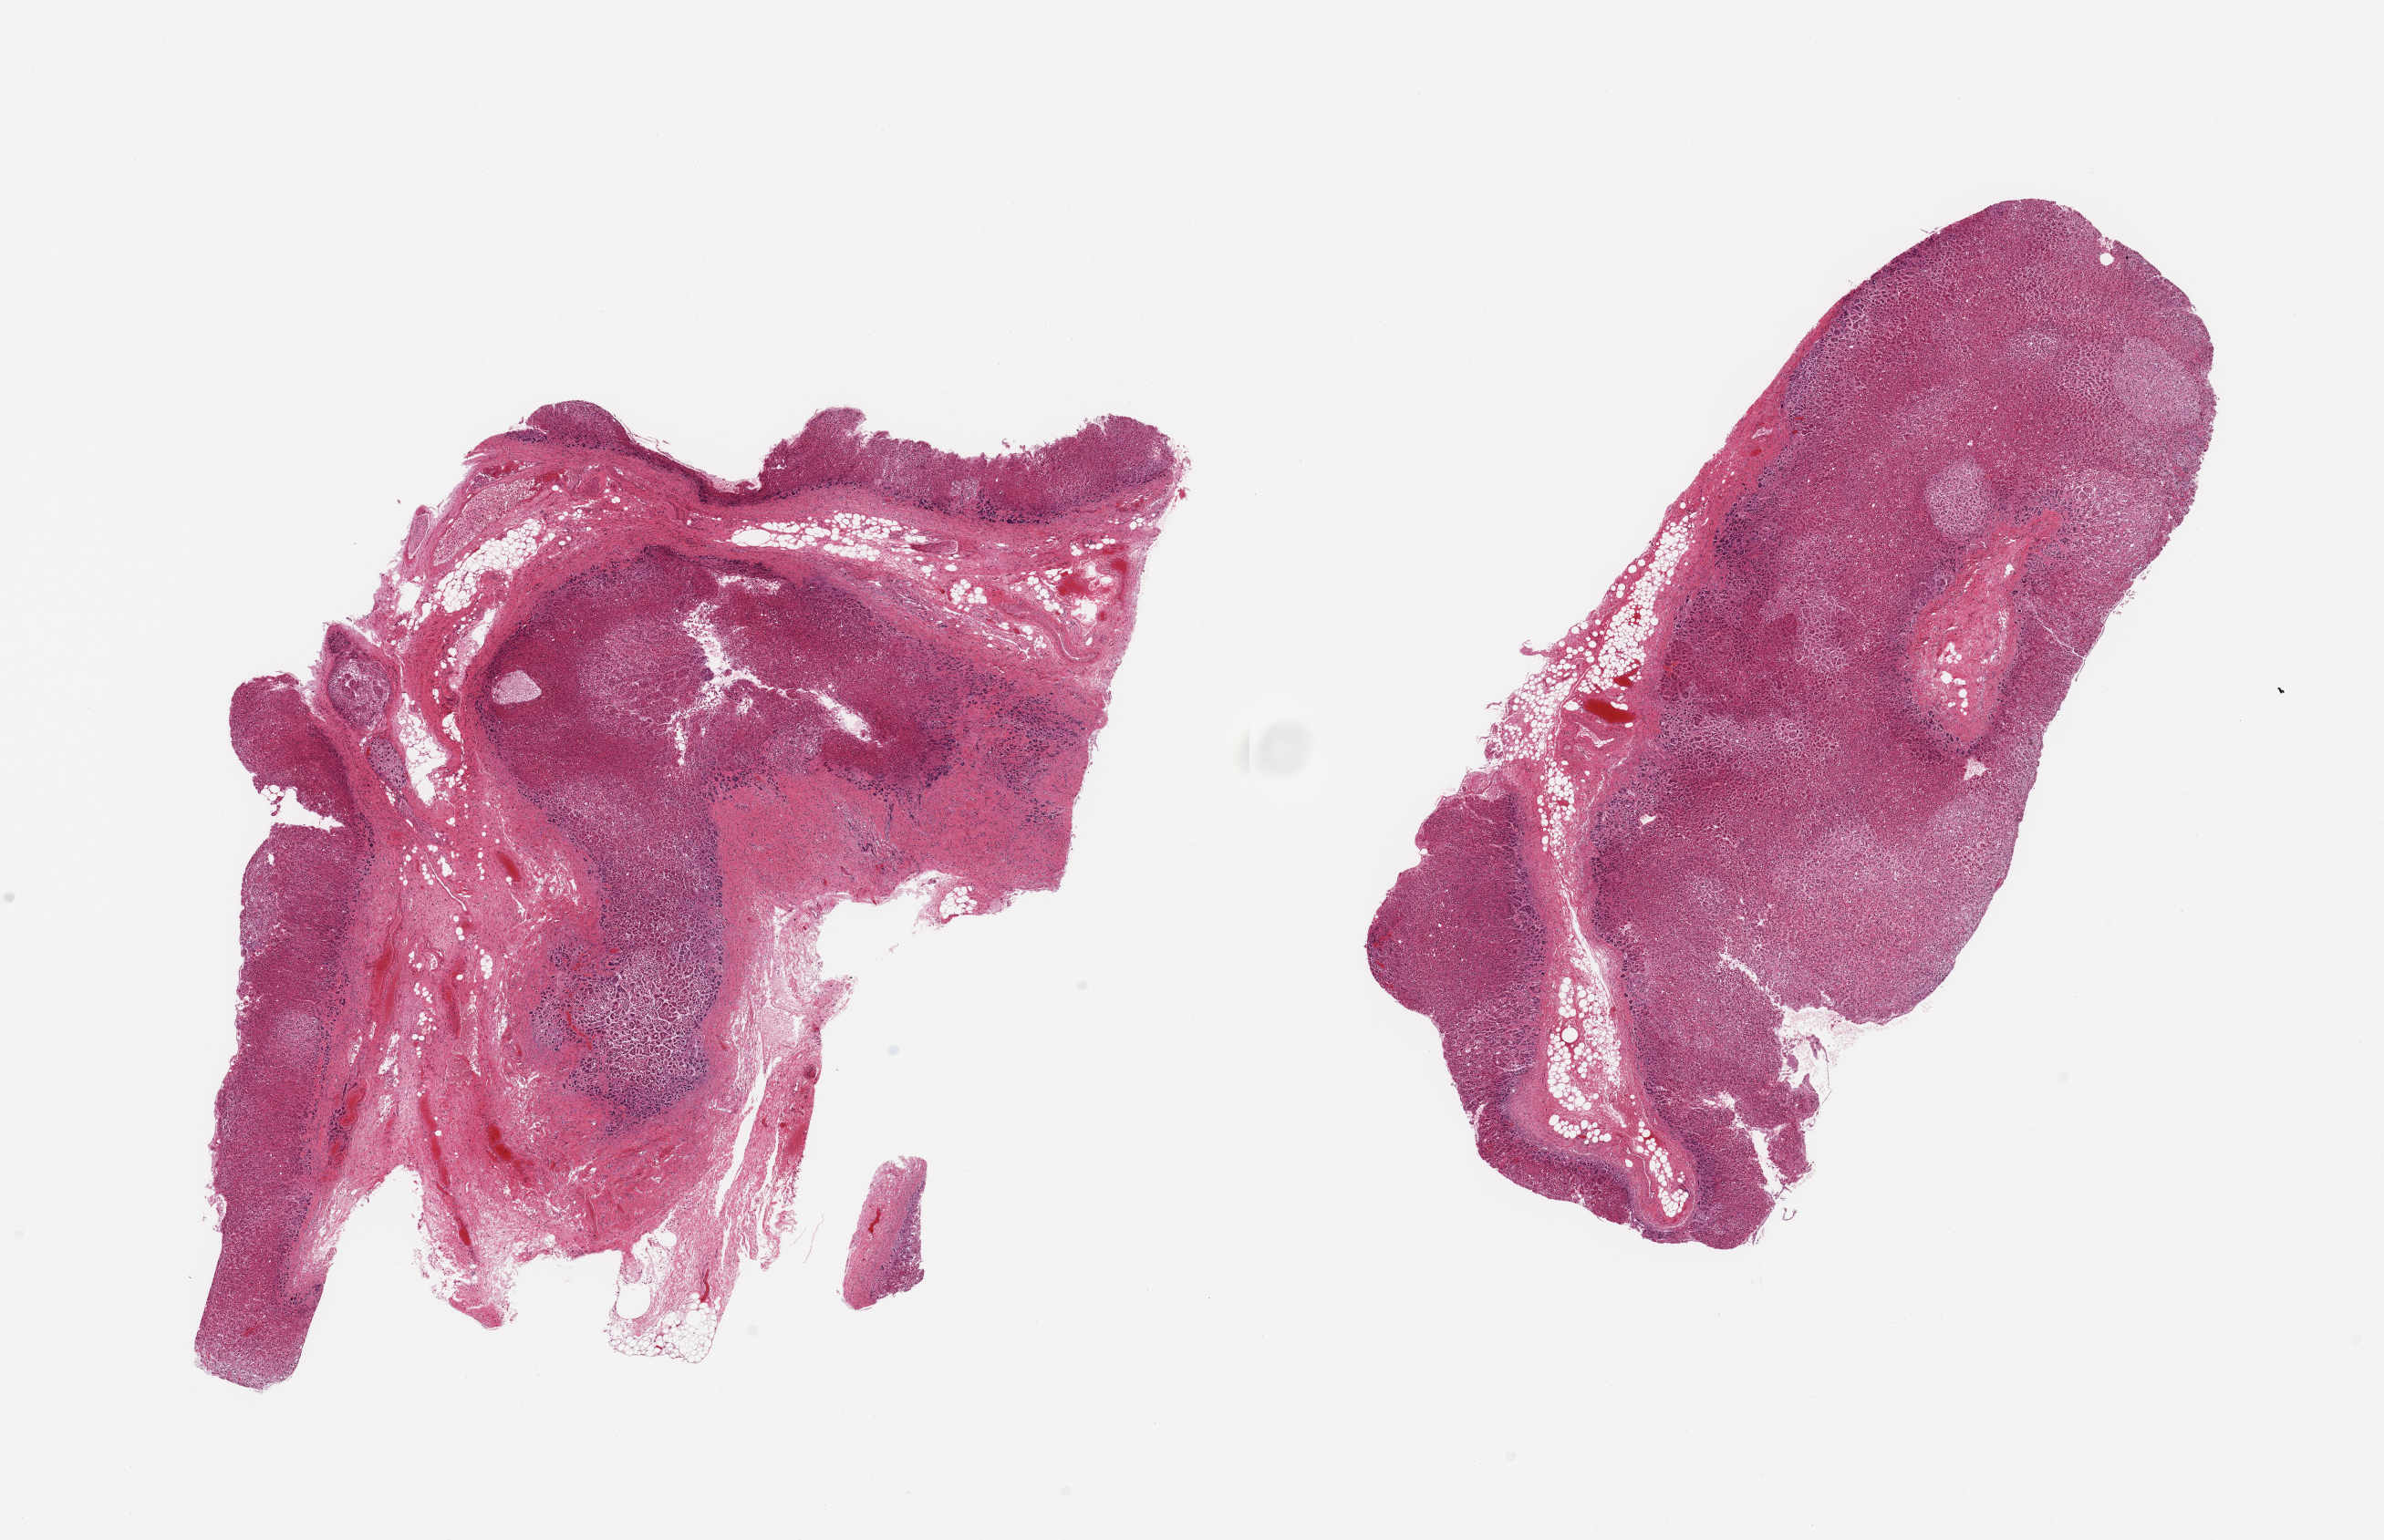
H&E whole-slide image — shown as a low-resolution overview of the whole scanned area (about 20.7 x 13.4 mm, acquisition: 20x scan). PAXgene-fixed paraffin-embedded (PFPE) section. Section of adrenal gland (target tissue). Tissue donor sample.
* review note (as recorded): 2 pieces; 20 & 10% internal fat